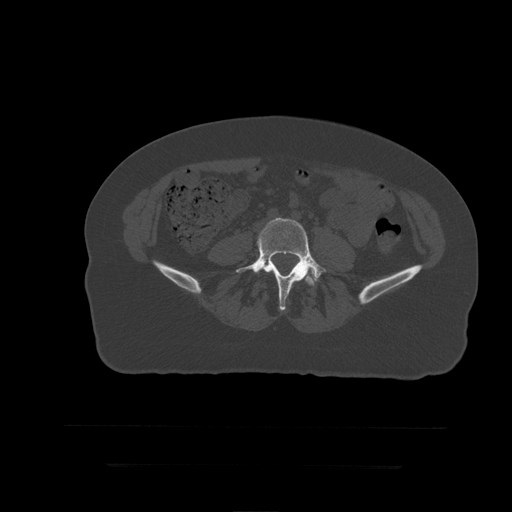
CT including the spine, one axial slice. Slice 76 of 399 in the series (ordered by position). 120 kVp. Bone window (W 1800 / L 400 HU). 1.25 mm slice thickness. 512 × 512 image matrix. Patient age 41 years. Case-level facts recorded for this patient, not image findings: primary cancer: breast.
Outlined on this slice (semi-automatic segmentation, software-assisted and operator-edited):
- L5 vertebra: bounding box (x1, y1, x2, y2) in pixels: (236, 219, 327, 311)